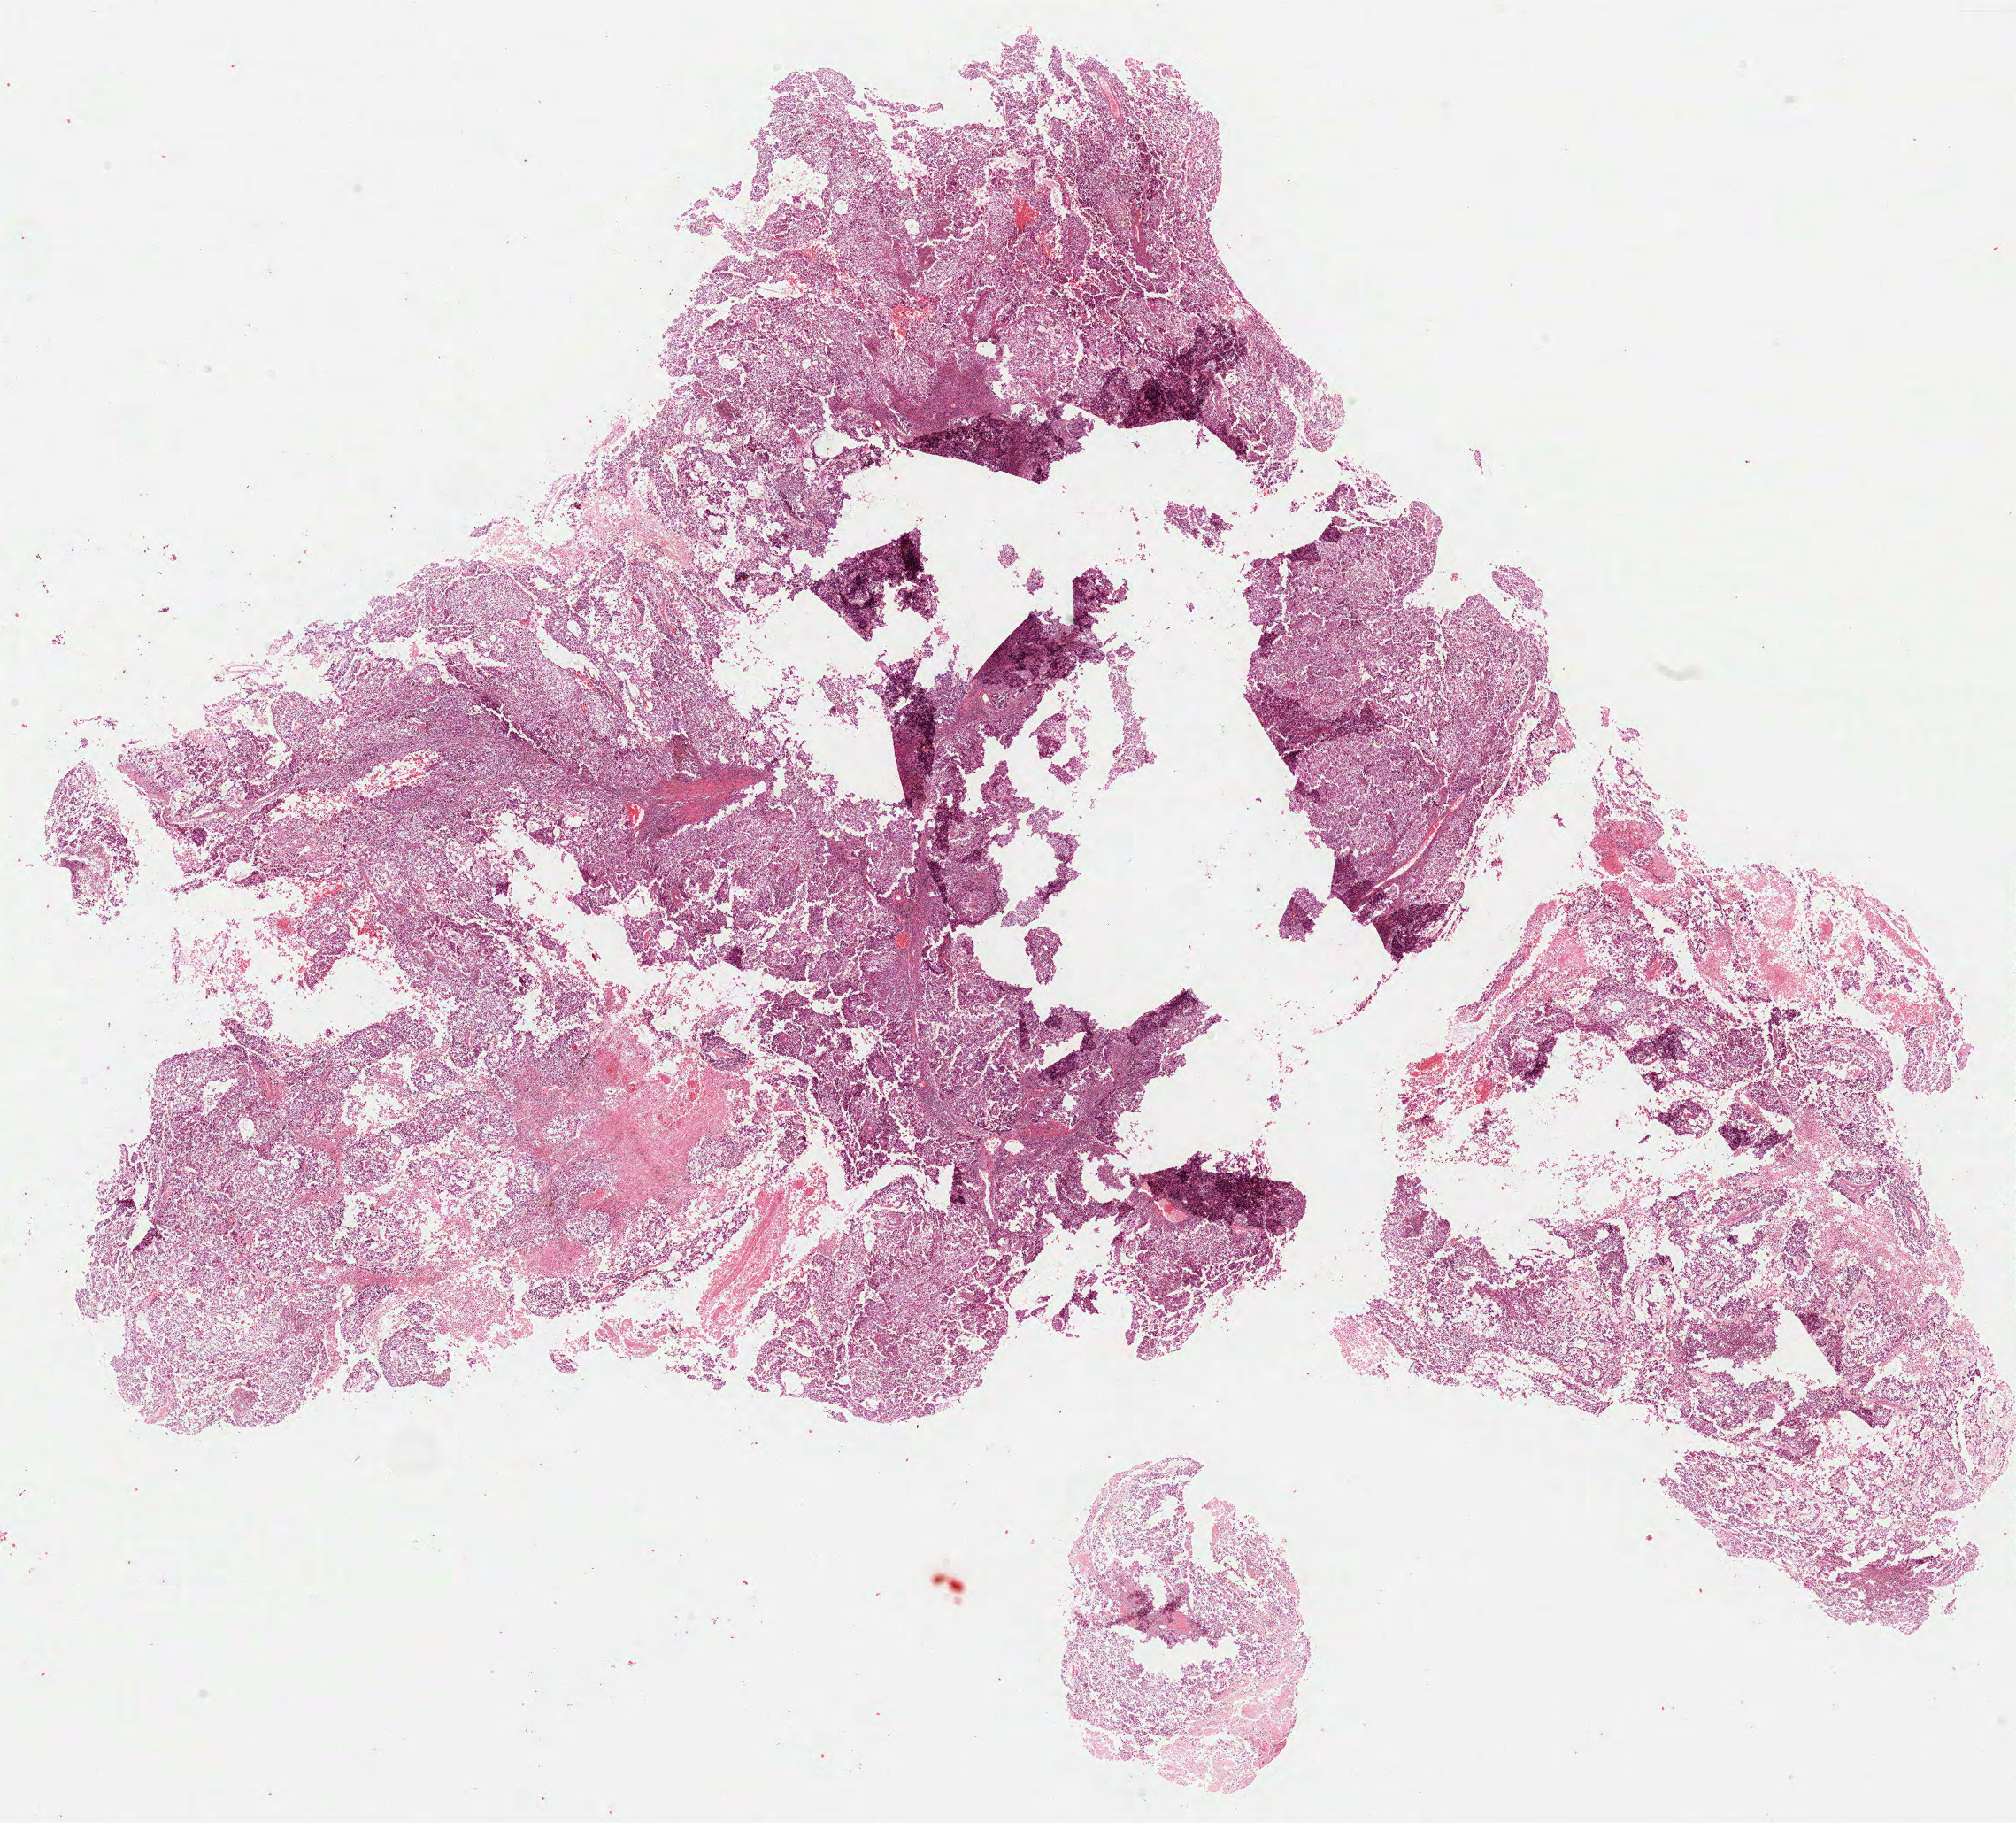
Whole-slide histology image, H&E — shown as a low-resolution overview of the whole scanned area (about 18.4 x 16.6 mm). Formalin-fixed paraffin-embedded (FFPE) diagnostic section. Lung, primary tumour sample. Male patient; age at initial diagnosis 59 years.
Pathologic diagnosis: Squamous cell carcinoma, NOS (upper lobe, lung). AJCC pathologic stage: IIA (7th edition). TNM: T1b N1 M0.